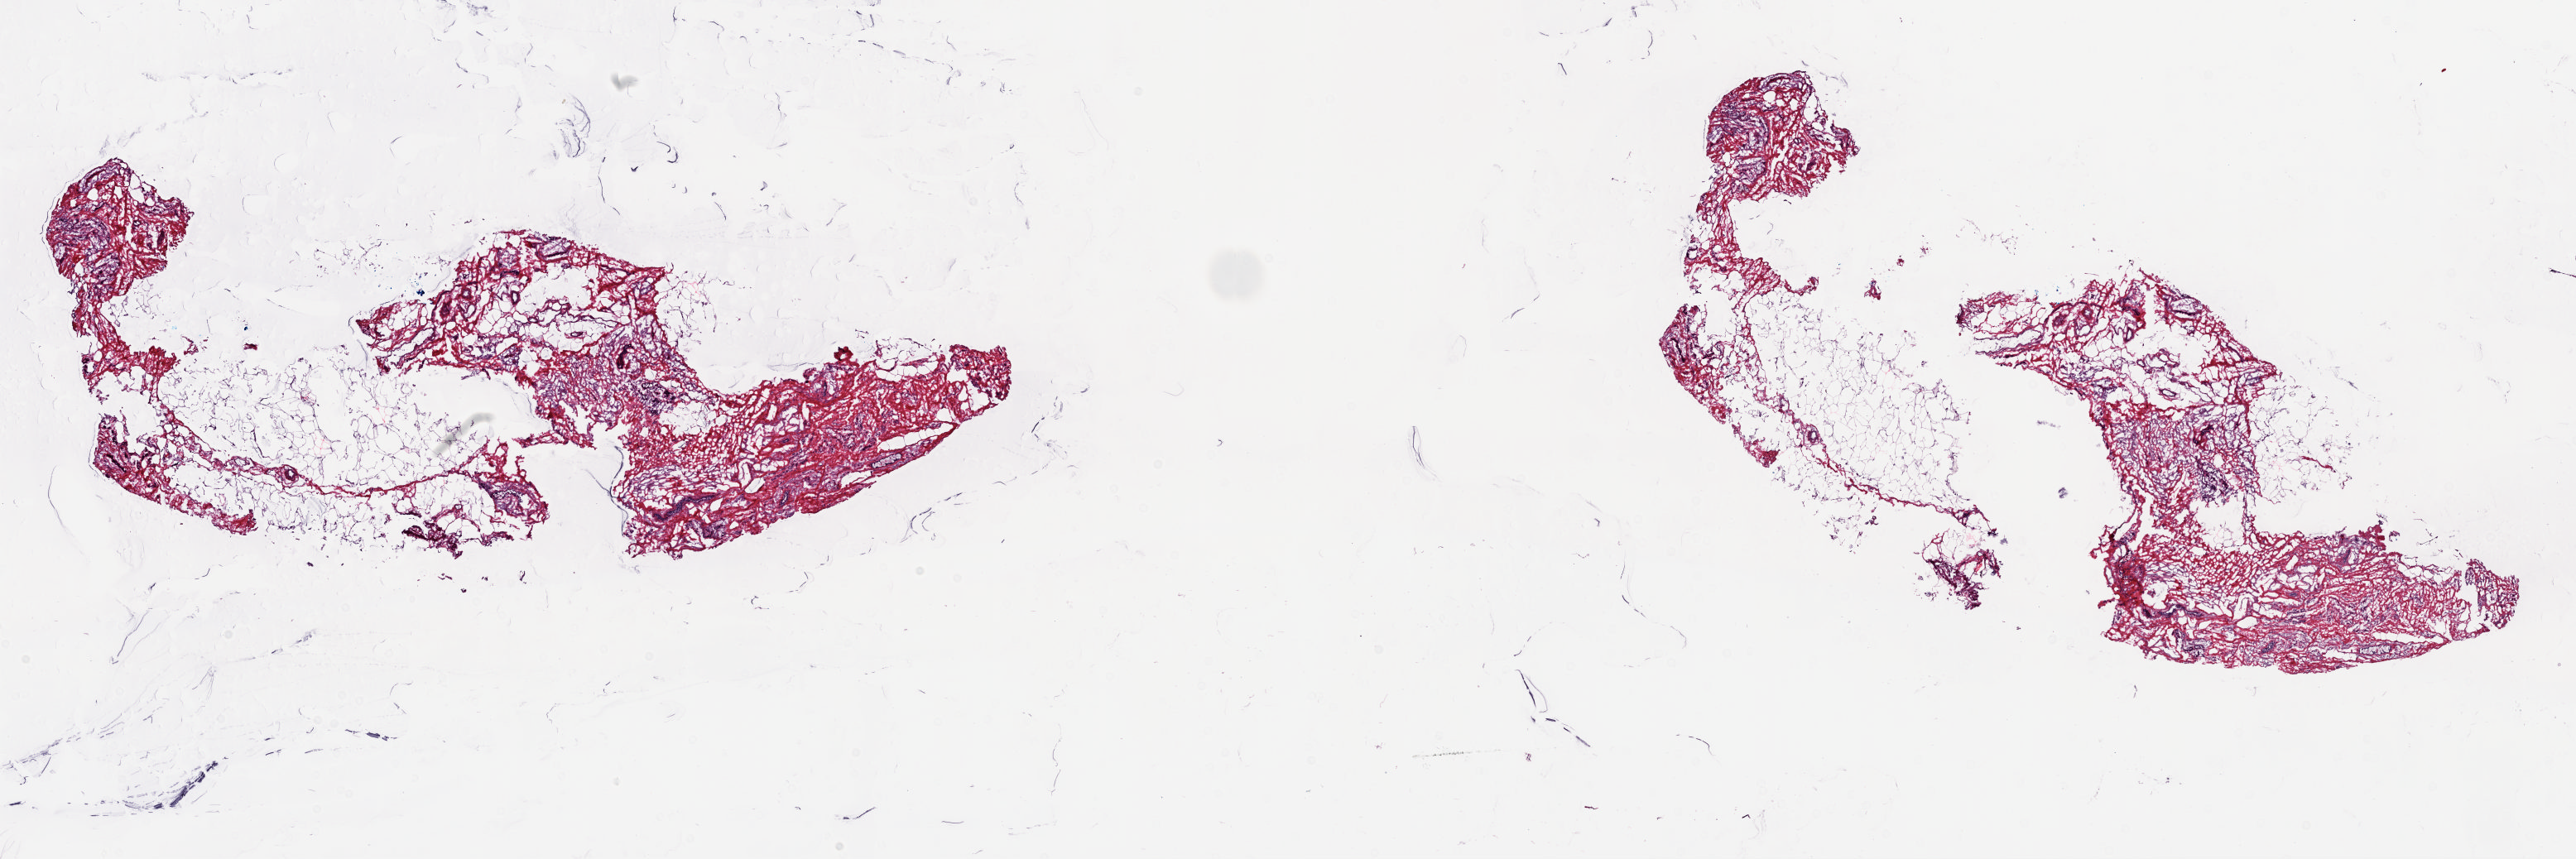
Digitized Hematoxylin and eosin (H&E) stained tissue section (whole slide), whole scanned area (about 24.6 x 8.2 mm) shown as a low-resolution overview. Frozen section from the top of the tissue portion. Breast, solid tissue normal (non-tumour tissue) sample. Female, age 76 years at initial diagnosis. Composition of this section per pathologist review: tumour cells 0%, tumour nuclei 0%, normal cells 25%, stromal cells 75%, necrosis 0%. Infiltration values recorded for this section: lymphocyte infiltration 0%, monocyte infiltration 0%, neutrophil infiltration 0%.
* this section: solid tissue normal (non-tumour) sample from the same patient
* patient diagnosis: Lobular carcinoma, NOS